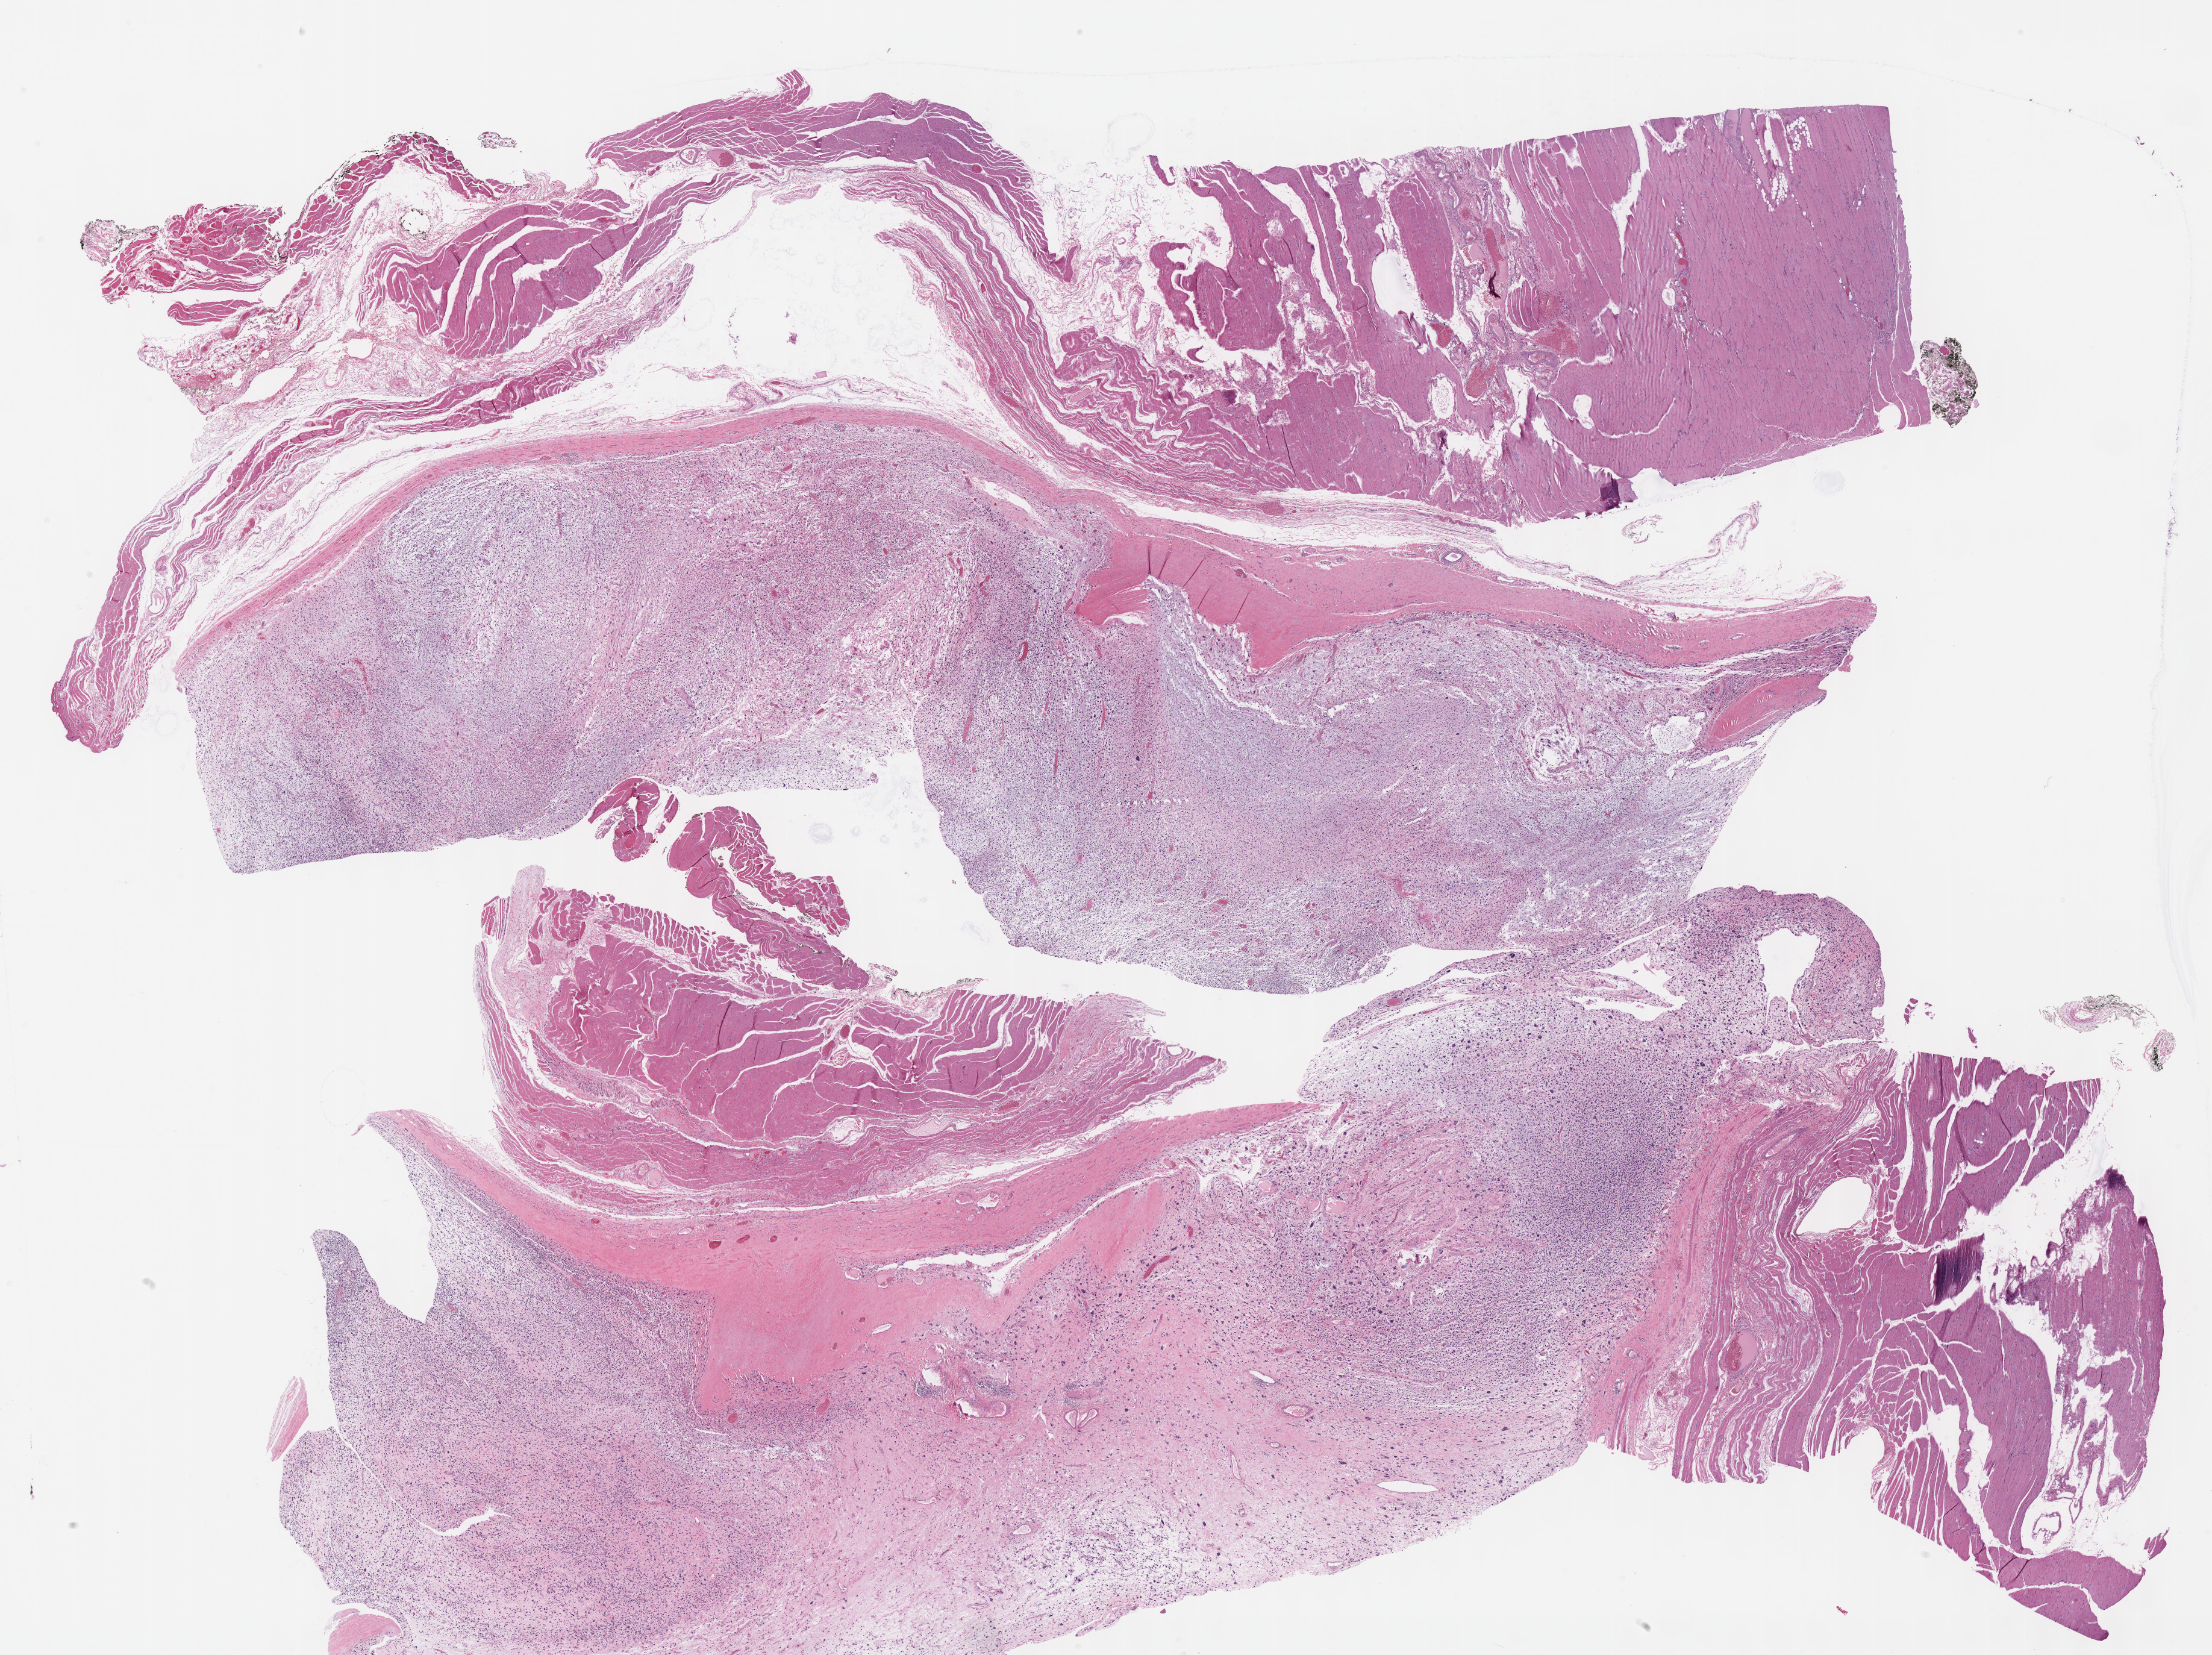
Hematoxylin and eosin (H&E) stained whole-slide image — whole scanned area (about 29.7 x 22.2 mm, slide scanned at 40x) shown as a low-resolution overview, formalin-fixed paraffin-embedded (FFPE) diagnostic section, connective, subcutaneous and other soft tissues, primary tumour sample. Female patient; age at initial diagnosis 83 years.
Histologic diagnosis: Fibromyxosarcoma (connective, subcutaneous and other soft tissues of lower limb and hip).